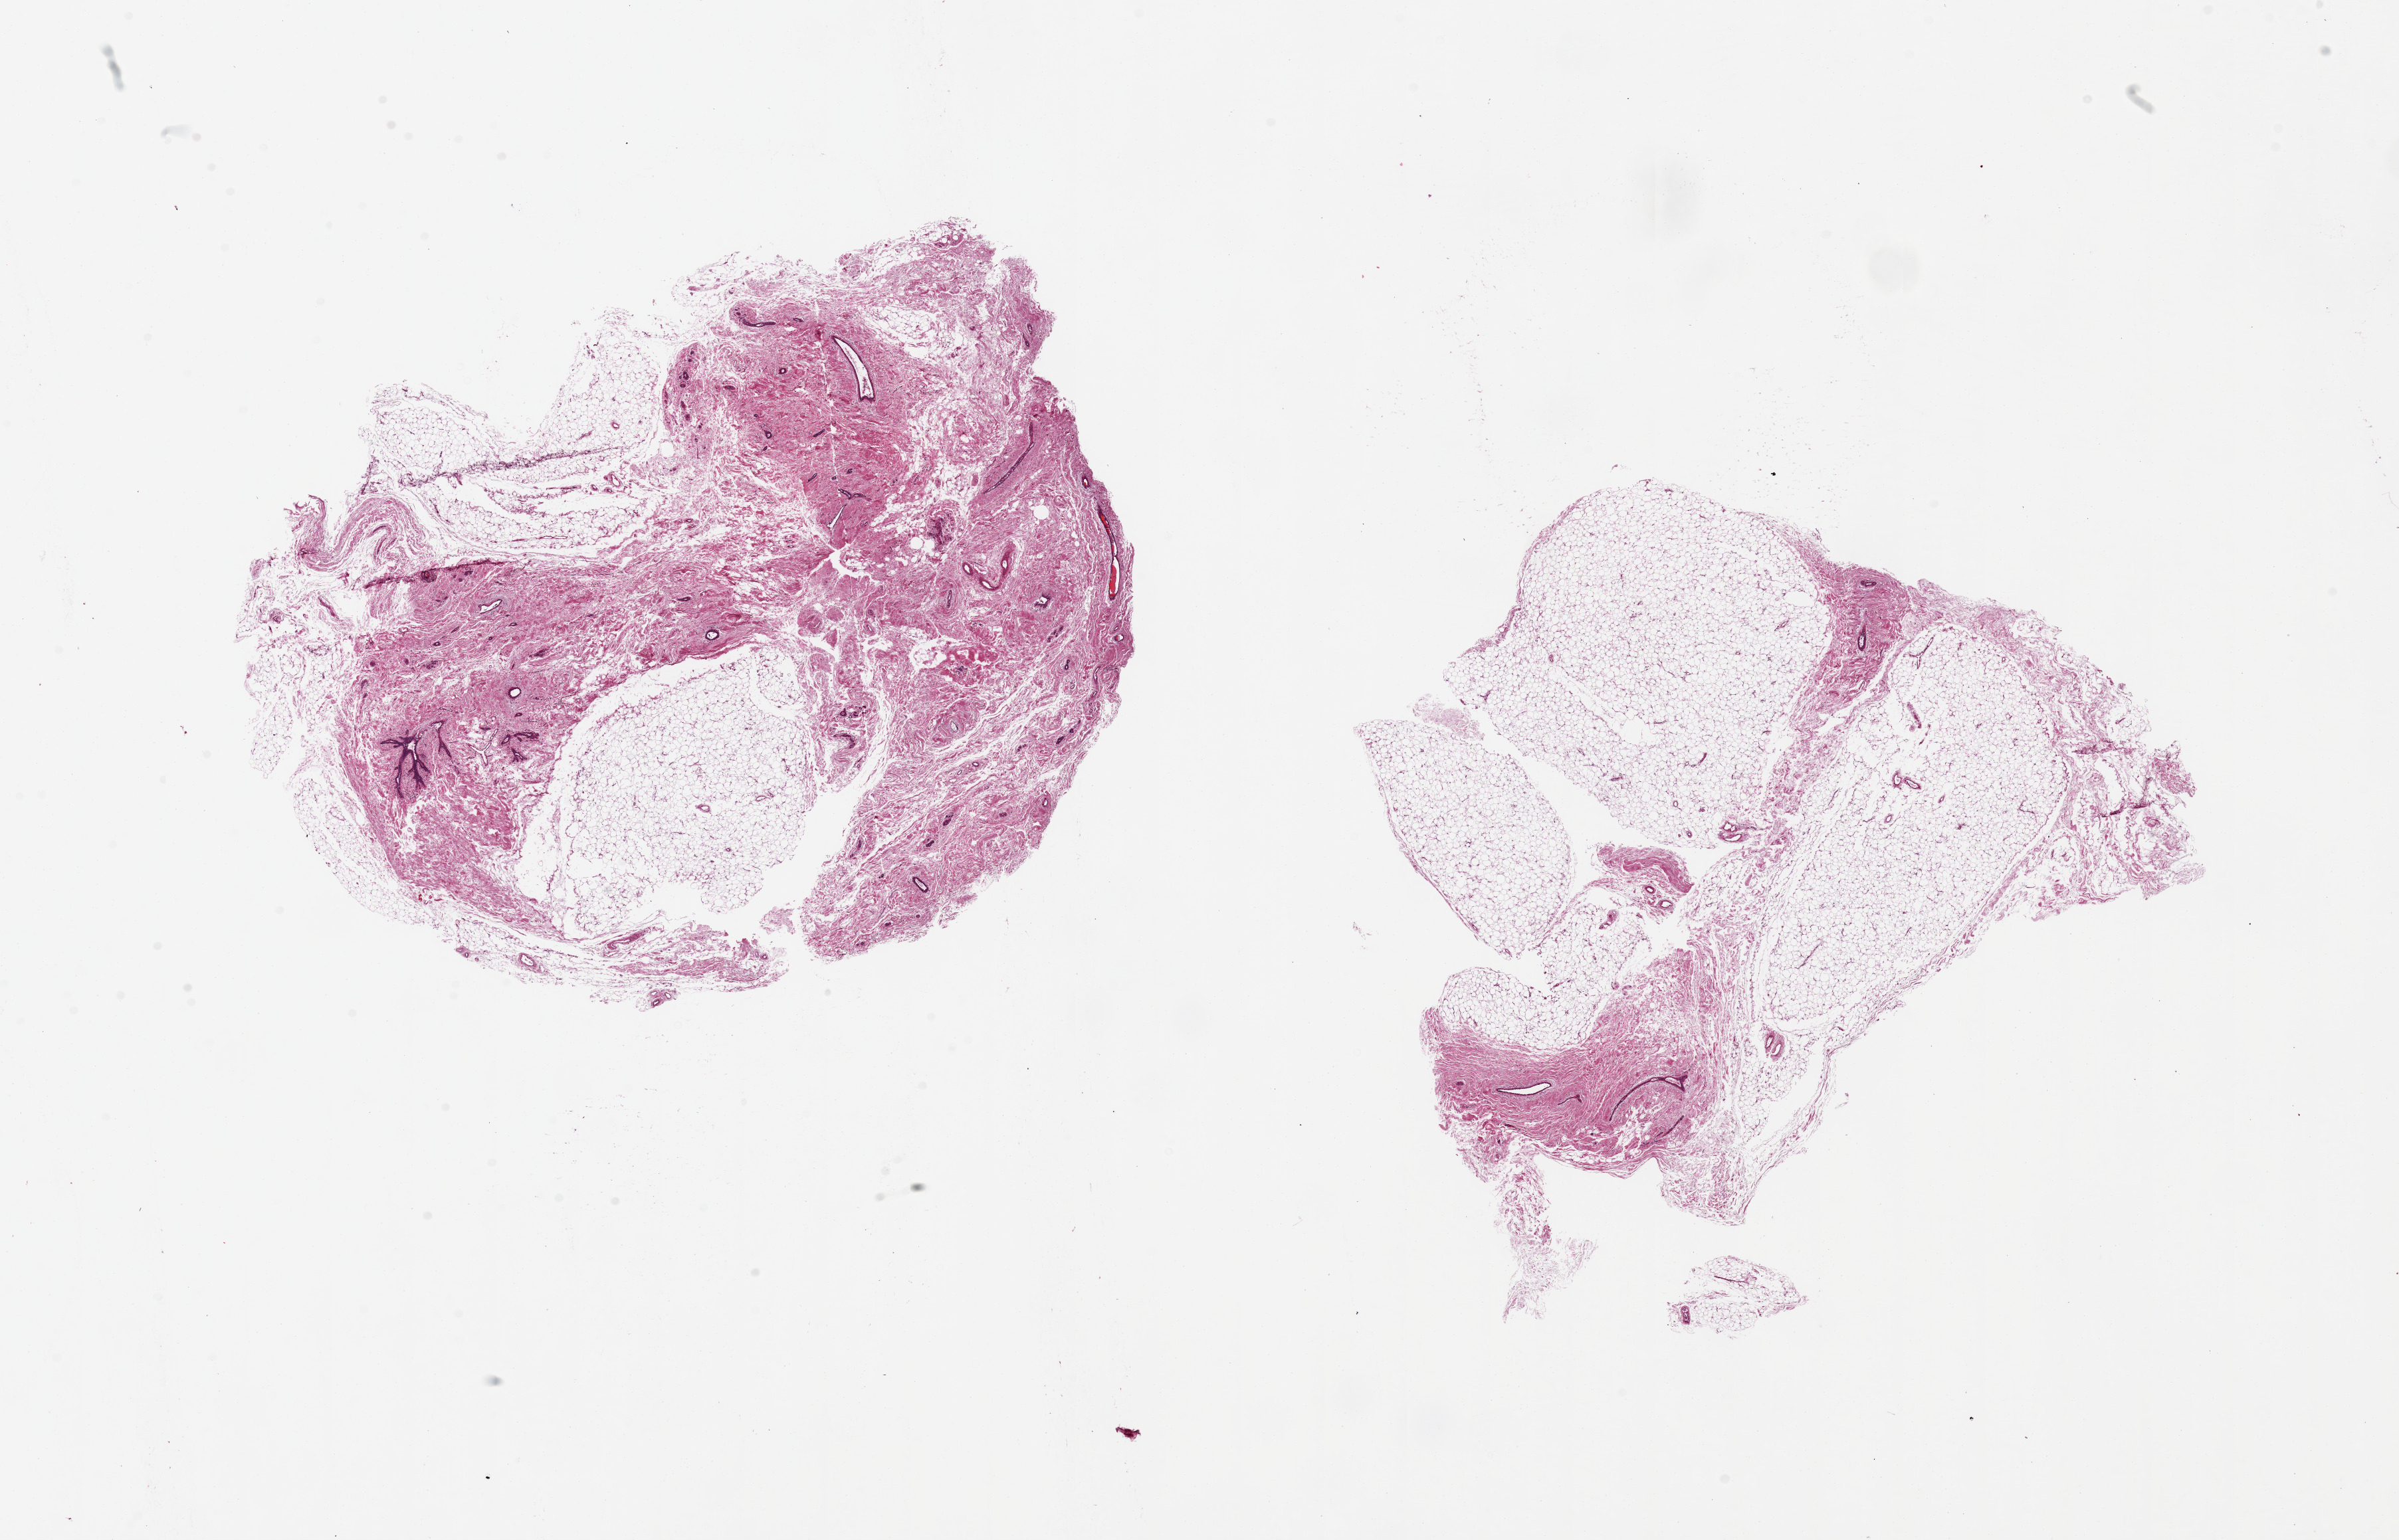
Digitized H&E-stained section, low-resolution overview of the scanned area, about 28.5 x 18.3 mm; PAXgene-fixed paraffin-embedded (PFPE) section; target tissue: breast; tissue donor sample. Donor sex: female.
Reviewer comment on this tissue sample: 2 pieces, 11x9 & 11x9mm; ducts, no lobules, atrophic.